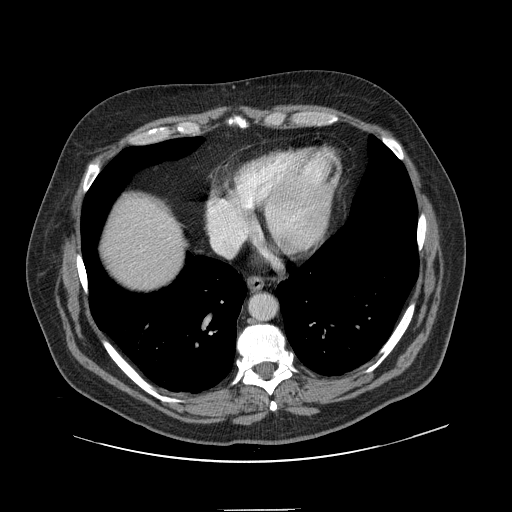
Contrast-enhanced abdominal CT, one axial slice. 120 kVp. Intravenous contrast given. Soft-tissue window (W 400 / L 40 HU). 2.5 mm slice thickness. 512 × 512 image matrix, field of view 451 × 451 mm. Male patient, age 61 years. Case-level facts recorded for this patient, not image findings: diagnosis: colorectal cancer liver metastases, imaged before liver resection; multiple liver metastases: yes; largest metastasis: 2.6 cm.
Annotated regions visible in this slice (expert manual segmentation):
- liver: bounding box [x1, y1, x2, y2] px = [104, 197, 184, 292]
- planned liver remnant (the part of the liver to remain after resection): [104, 196, 184, 292]